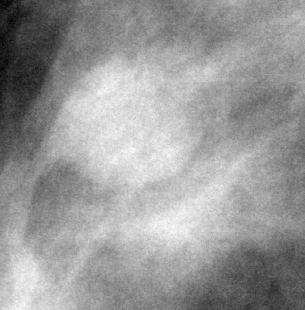
Crop from a digitized film mammogram around one marked abnormality, right breast, MLO view, BI-RADS breast density category 2 (scale 1–4).
- Finding: mass, shape oval, margins circumscribed; BI-RADS assessment category 3; subtlety rating 4 on a 1 (subtle) to 5 (obvious) scale; pathology (as recorded): benign.